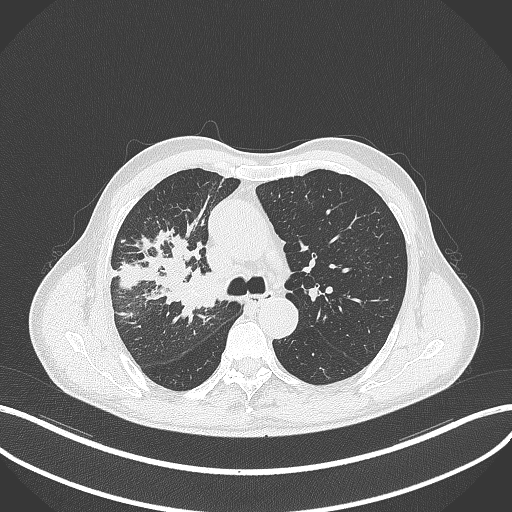
Chest CT, one axial slice; position 326 of 490 along the scan axis; lung window (W 1500 / L -600 HU); 512 × 512 image matrix. Patient: male, 69 years. Case-level facts recorded for this patient, not image findings: clinical TNM (as recorded): T2a N0 M0.
Outlined on this slice (bounding box drawn by a radiologist):
- lung tumour (recorded histology: adenocarcinoma): bounding box (x1, y1, x2, y2) in pixels: (176, 264, 219, 318)